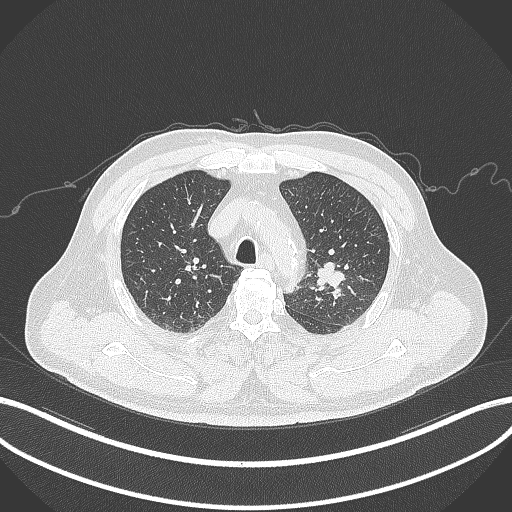
Chest CT, one axial slice. Slice 233 of 286 in the series (ordered by position). Reconstruction kernel B70f. 120 kVp. Lung window (W 1500 / L -600 HU). 1 mm slice thickness. 512 × 512 image matrix, field of view 400 × 400 mm. Male patient, age 67 years. From the clinical record (not read from this slice): clinical TNM (as recorded): T2a N1 M0.
Outlined on this slice (bounding box drawn by a radiologist):
- lung tumour (recorded histology: adenocarcinoma): bounding box (x1, y1, x2, y2) in pixels: (314, 258, 351, 295)